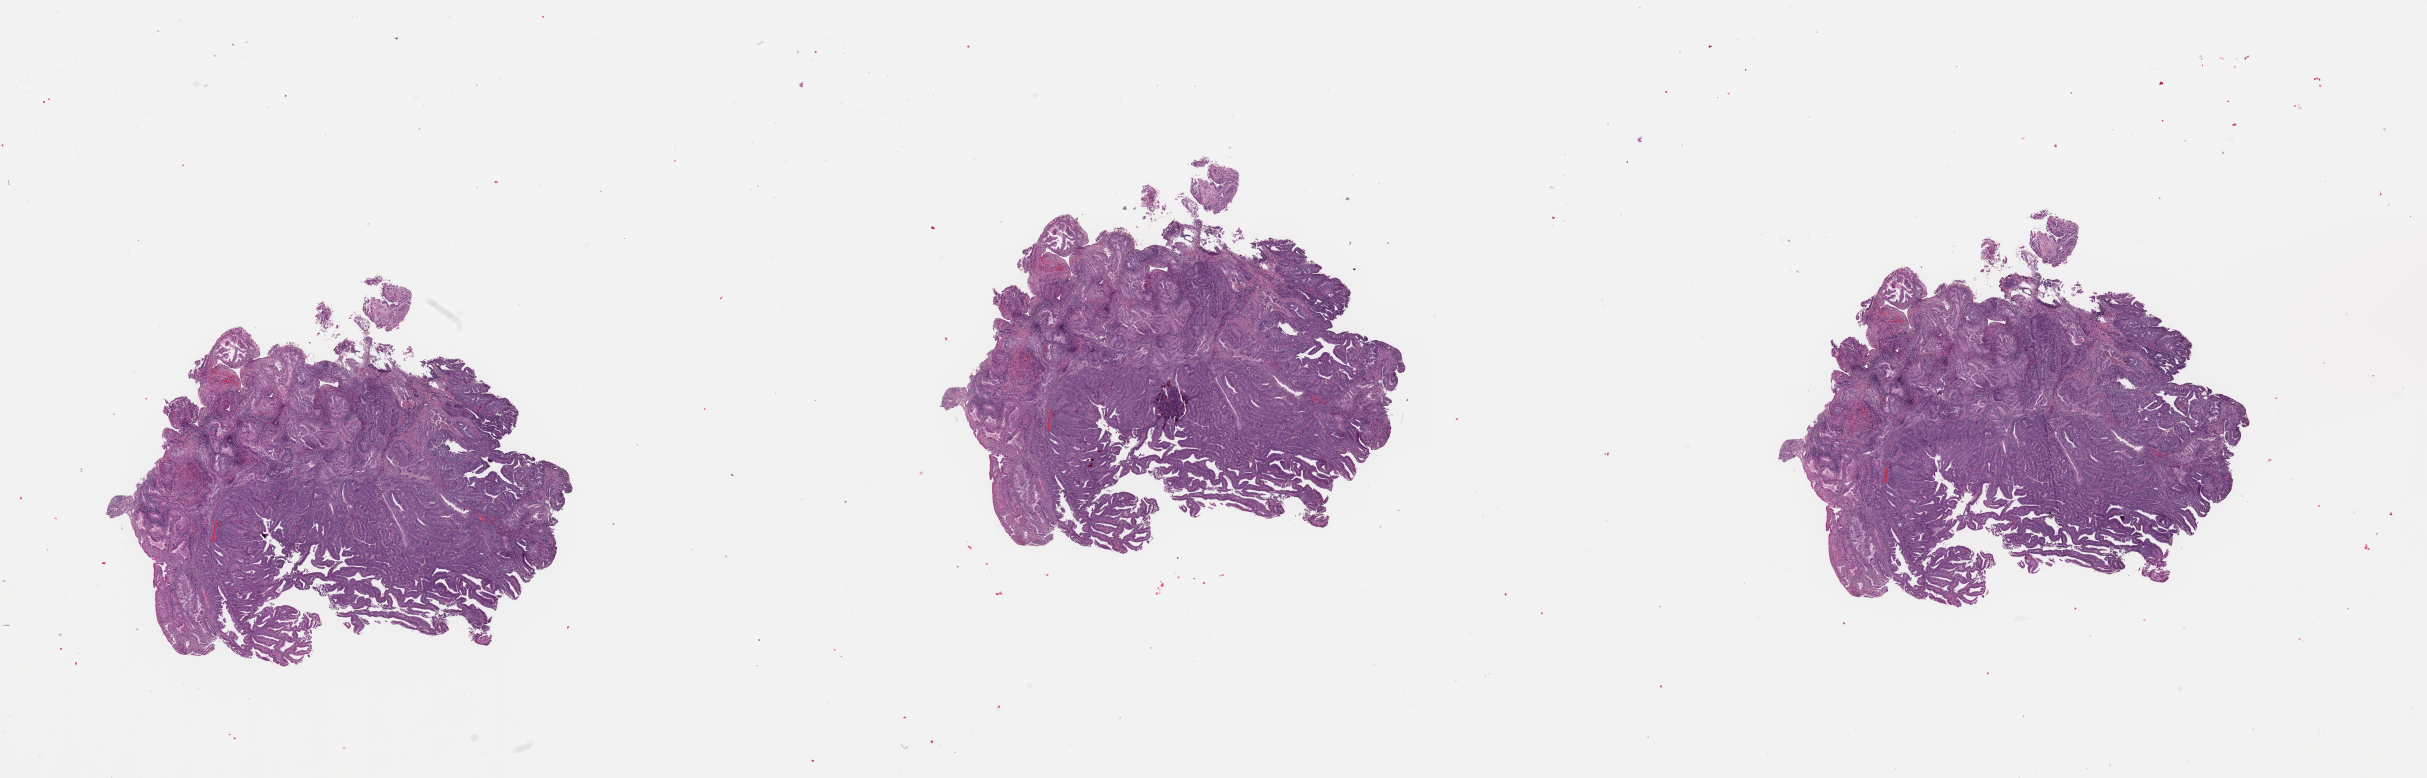
H&E whole-slide image — low-resolution overview of the scanned area, about 38.4 x 12.3 mm (slide scanned at 20x), tumour tissue sample, sampled site: uterus. 39-year-old female patient. Histologic grade: G2 (moderately differentiated). Pathologist review of this section (percent, as recorded): tumour nuclei 90%, necrosis 0%.
AJCC pathologic stage: I. Diagnosis: Endometrioid adenocarcinoma, NOS.